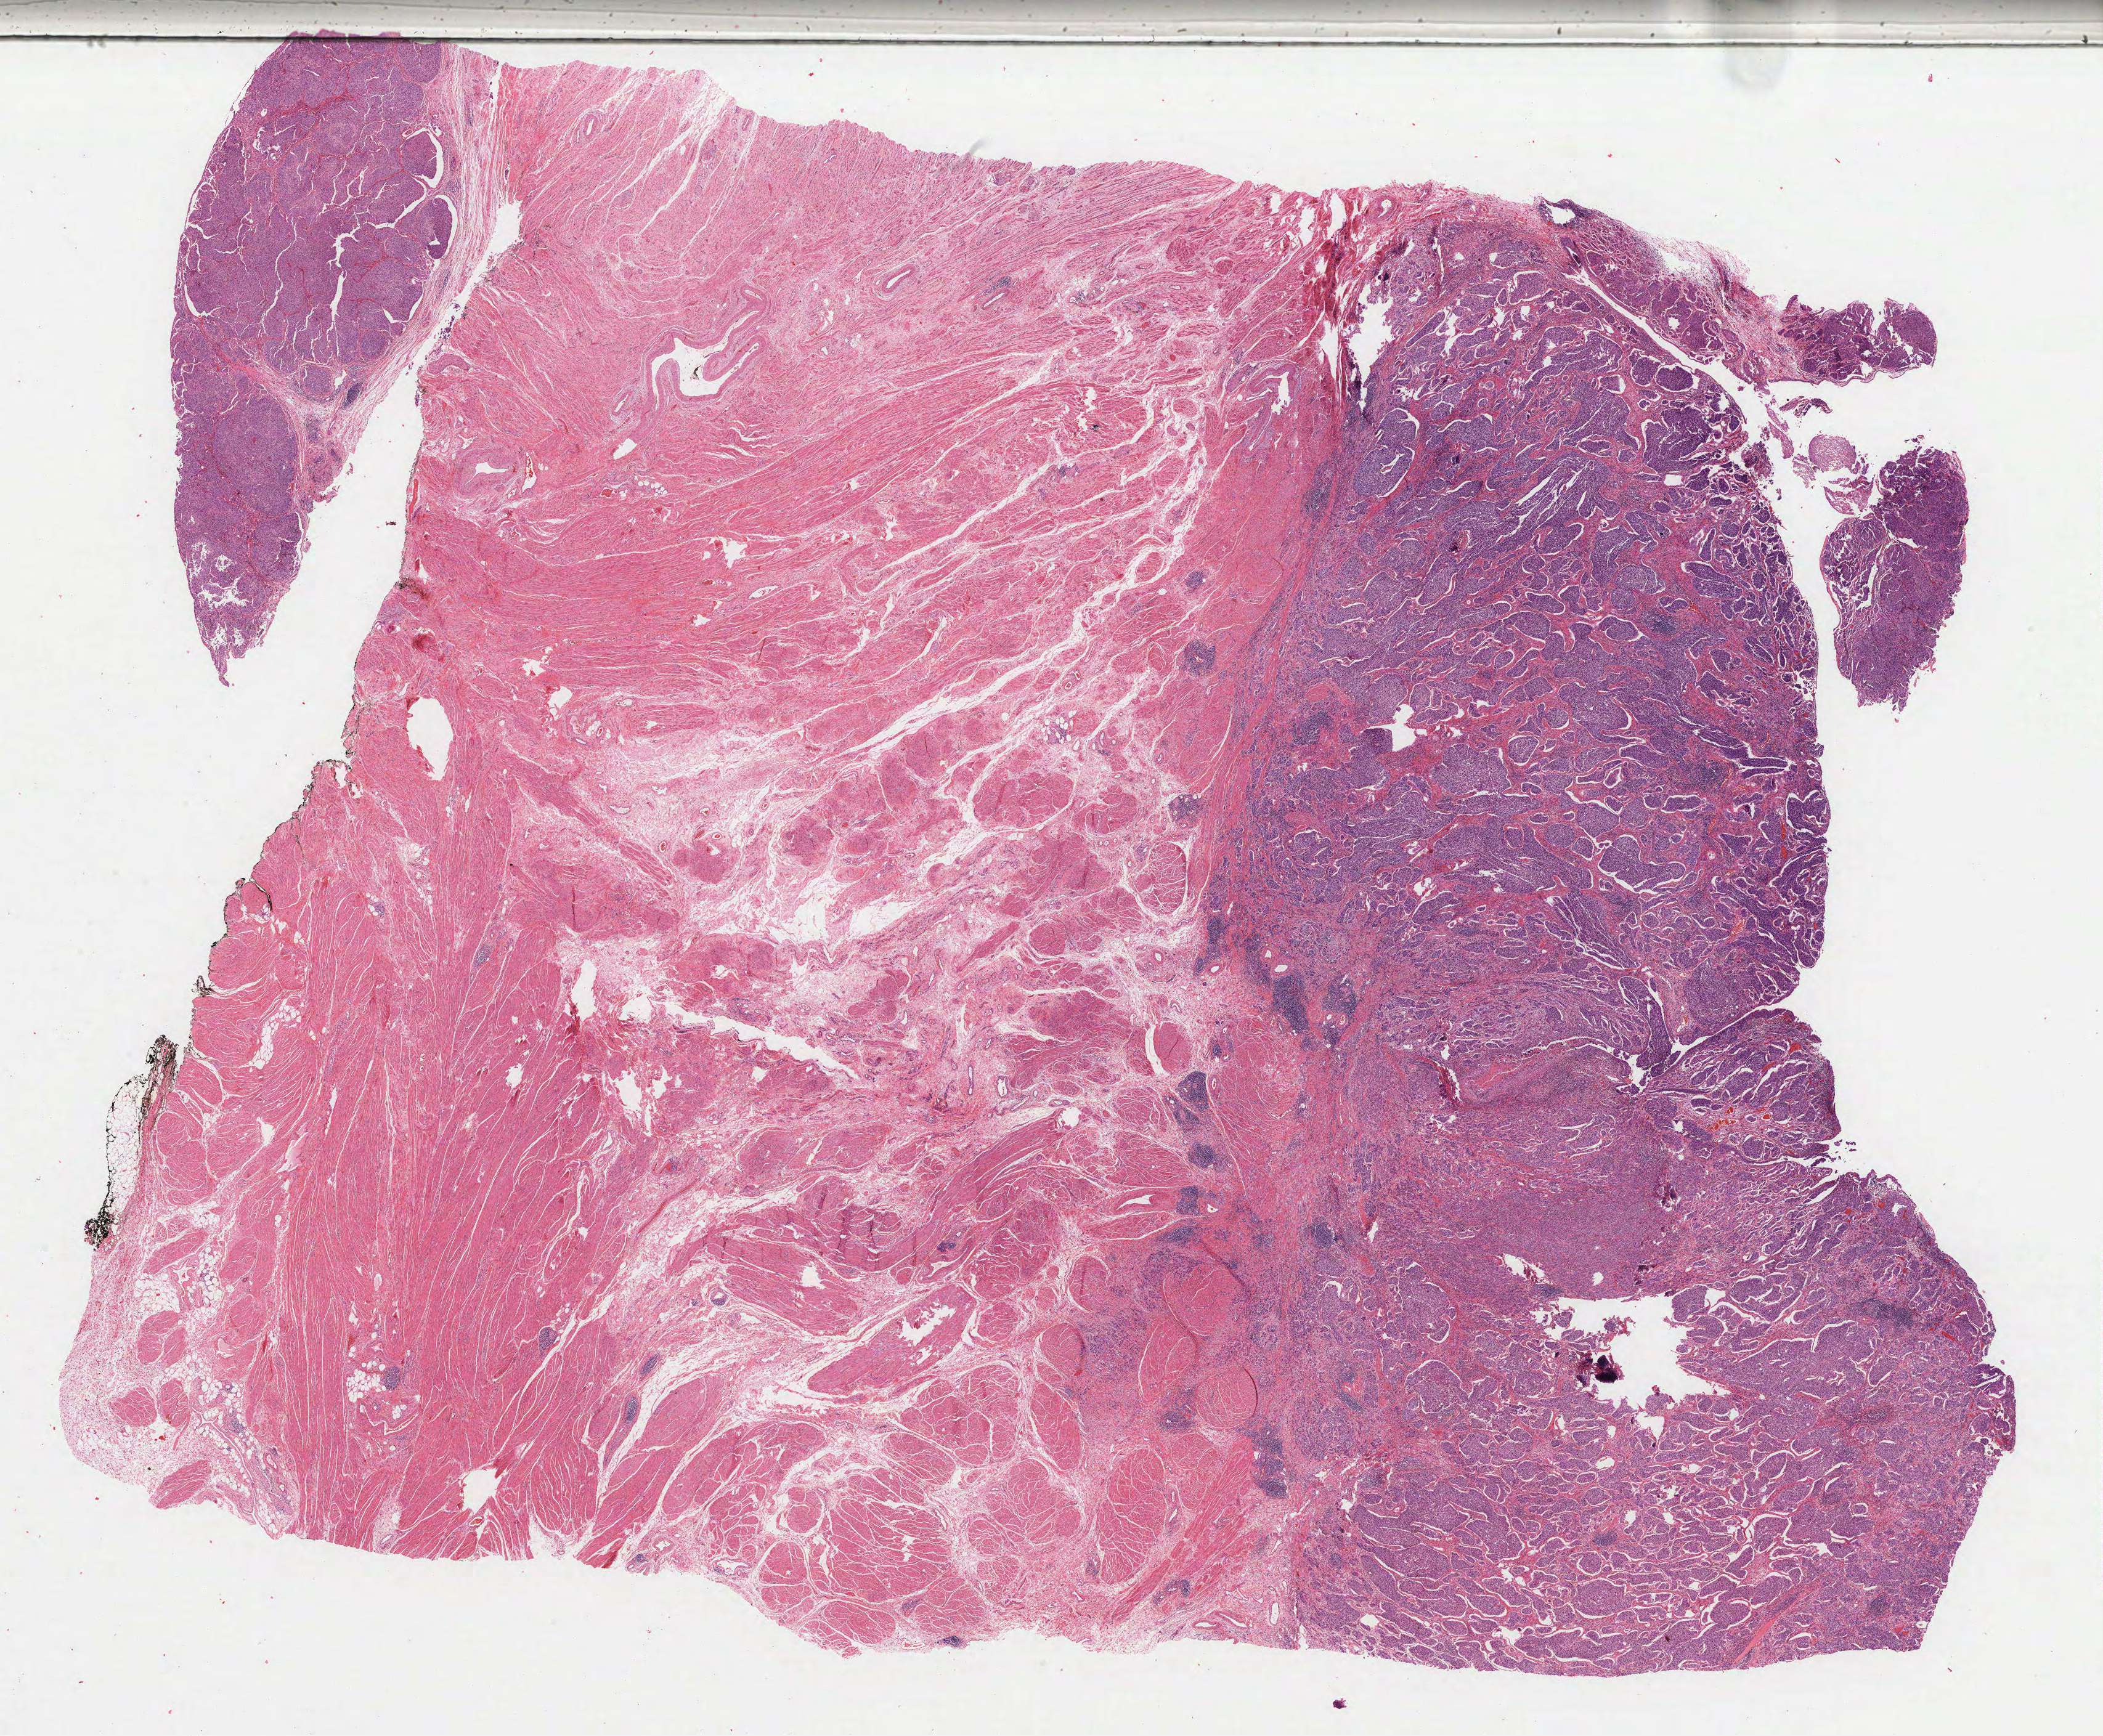
Digitized Hematoxylin and eosin (H&E) stained tissue section (whole slide) — low-resolution overview of the scanned area, about 27.1 x 22.4 mm (slide scanned at 40x), formalin-fixed paraffin-embedded (FFPE) diagnostic section, bladder, primary tumour sample. Patient: female, age at initial diagnosis 56 years. Histologic grade: high grade.
AJCC pathologic stage: IV (7th edition). Histologic diagnosis: Transitional cell carcinoma.